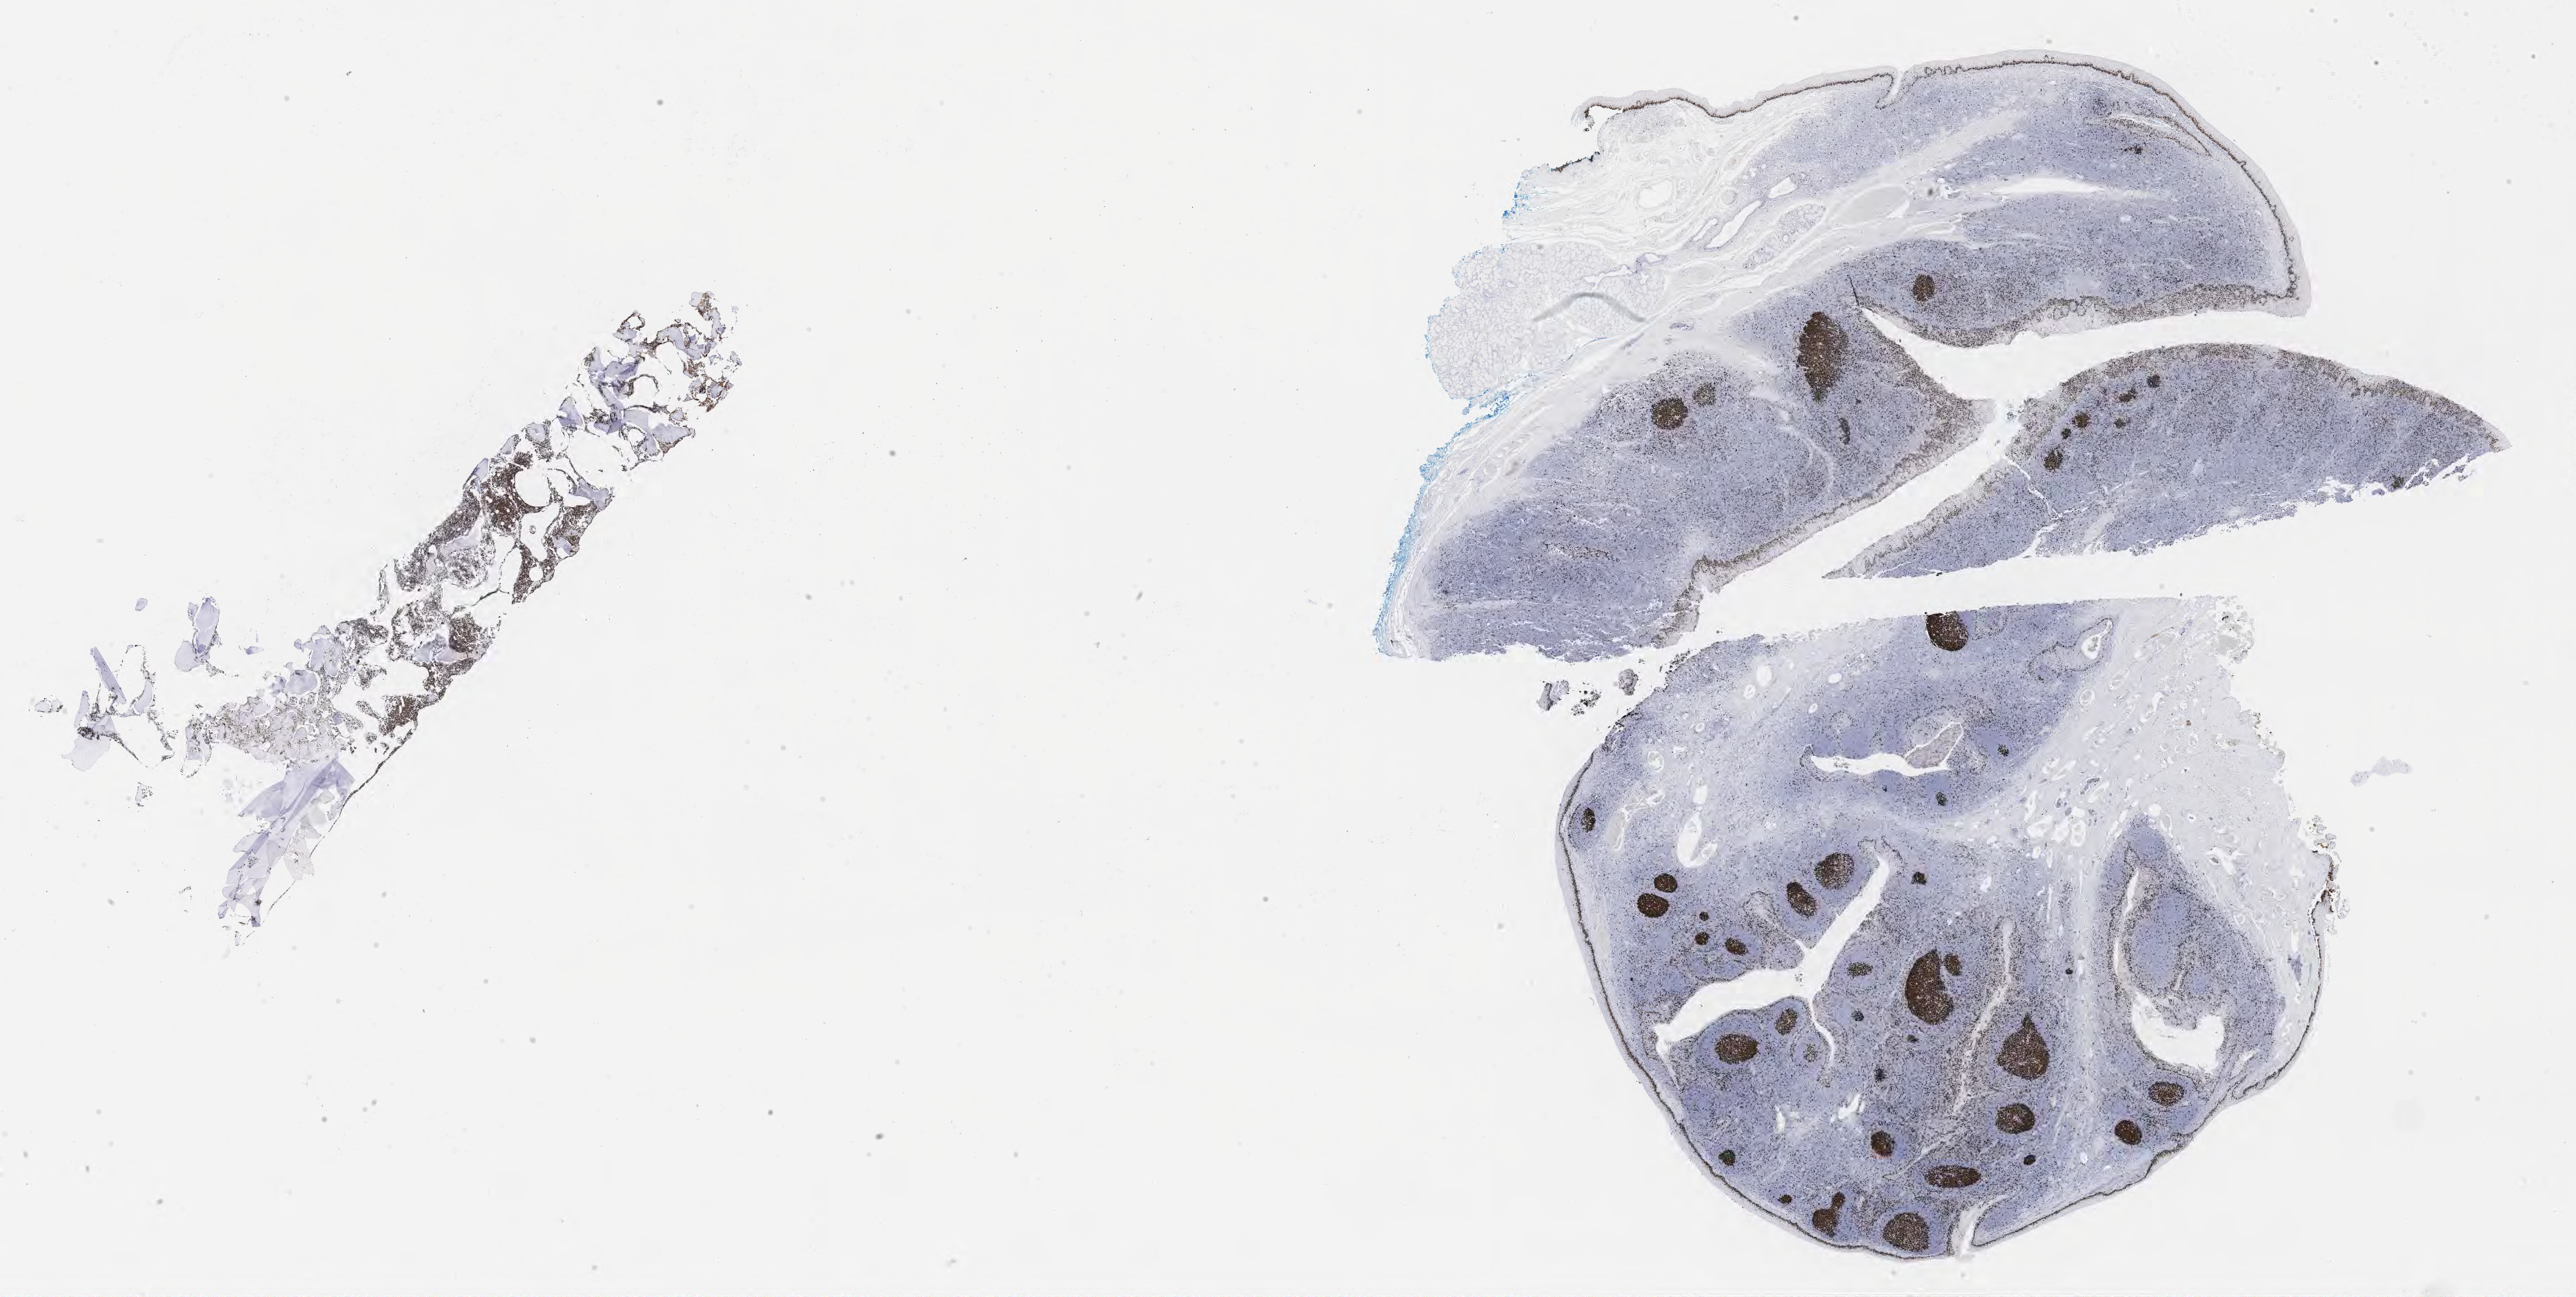
IHC for Ki-67, whole-slide image, low-resolution overview of the scanned area, about 30.2 x 15.2 mm, tumor tissue. Patient male; age 13 years.
Diagnosis: Burkitt lymphoma, NOS.